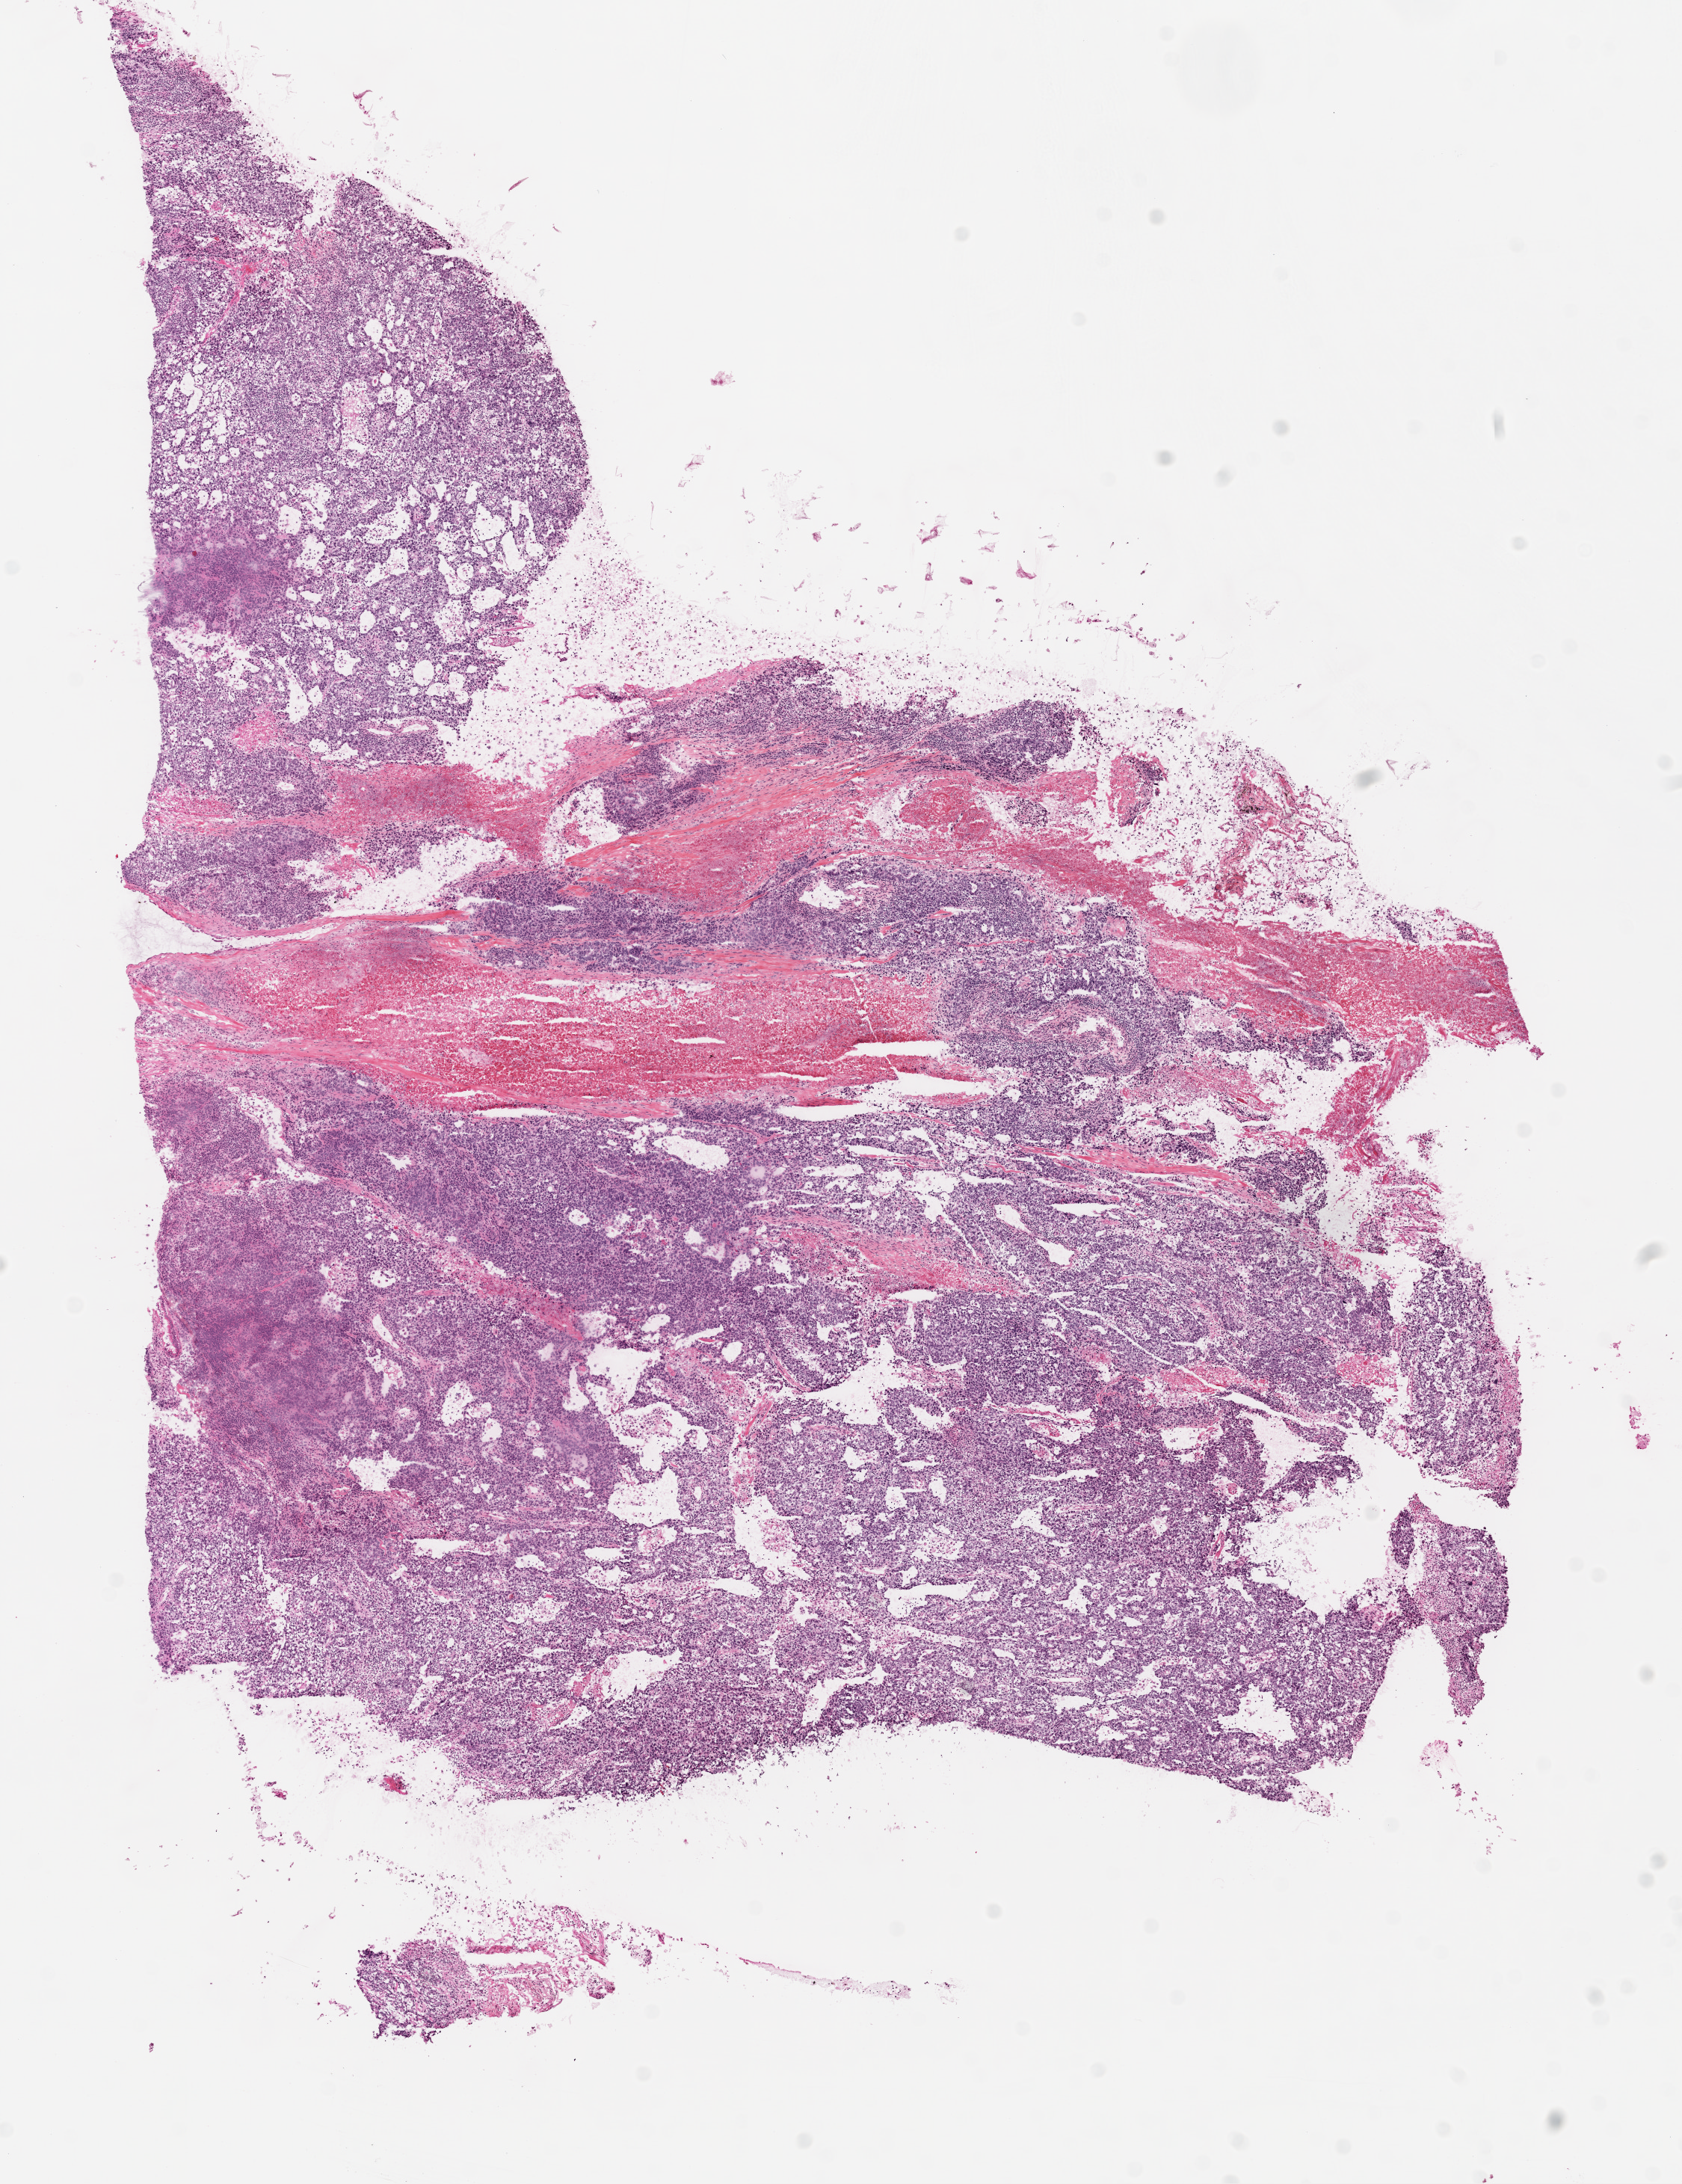
Digitized Hematoxylin and eosin (H&E) stained tissue section (whole slide) — low-resolution overview of the scanned area, about 9.0 x 11.7 mm (slide scanned at 20x), frozen section from the top of the tissue portion, lung, primary tumour sample. Male patient; age at initial diagnosis 56 years. Composition of this section per pathologist review: tumour cells 80%, tumour nuclei 75%, normal cells 5%, stromal cells 15%, necrosis 10%.
• laterality: right
• AJCC pathologic stage: IA
• pathologic diagnosis: Squamous cell carcinoma, NOS (upper lobe, lung)